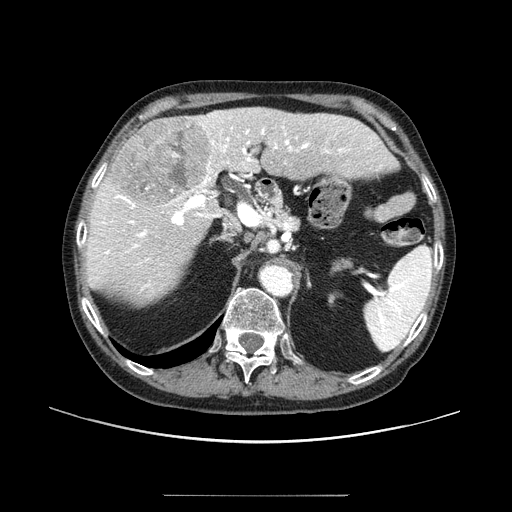
Contrast-enhanced abdominal CT (liver protocol), one axial slice. Position 56 of 91 along the scan axis. Reconstruction kernel STANDARD. One of 2 acquisitions stored at this slice position. Soft-tissue window (W 400 / L 40 HU). 2.5 mm slice thickness. 512 × 512 image matrix, field of view 400 × 400 mm. Case-level facts recorded for this patient, not image findings: diagnosis: hepatocellular carcinoma (patient treated with transarterial chemoembolisation; whether this scan precedes or follows treatment is not stated here); TNM stage (as recorded): Stage-I; Child-Pugh class: A; tumour differentiation: moderately differentiated.
Annotated regions visible in this slice (semi-automatic segmentation, software-assisted and operator-edited):
- liver parenchyma outside the tumour (the mass and vessels are separate outlines, so this box may not span the whole liver): box from (x=86, y=106) to (x=354, y=302) px
- mass: (x=111, y=117)–(x=213, y=211)
- liver vessels: (x=95, y=112)–(x=337, y=290)